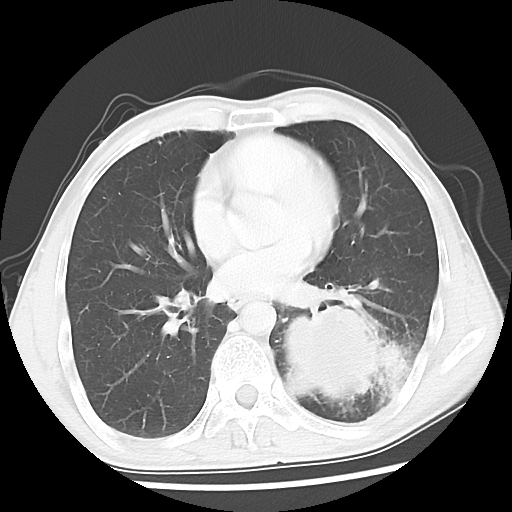
Chest CT, one axial slice. Slice 22 of 52 in the series (ordered by position). Reconstruction kernel LUNG. 120 kVp. Lung window (W 1500 / L -600 HU). 5 mm slice thickness. 512 × 512 image matrix, field of view 318 × 318 mm. Patient: male, 60 years. Case-level facts recorded for this patient, not image findings: clinical TNM (as recorded): T4 N0 M0.
Outlined on this slice (rectangle marked by the reading radiologist):
- lung tumour (recorded histology: squamous cell carcinoma): box from (x=275, y=295) to (x=411, y=419) px